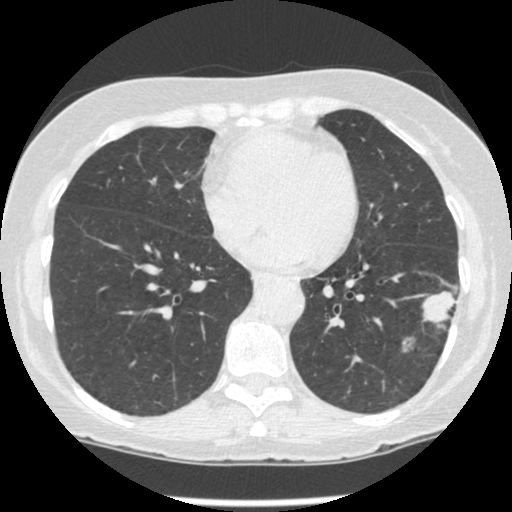
Low-dose screening chest CT, one axial slice. Position 97 of 247 along the scan axis. Reconstruction kernel STANDARD. Lung window (W 1500 / L -600 HU). 1.25 mm slice thickness. 512 × 512 image matrix, field of view 303 × 303 mm.
Outlined on this slice (manually delineated by an expert):
- lesion 1 (tumor, lower lobe of left lung): bounding box [x1, y1, x2, y2] px = [423, 291, 455, 326]